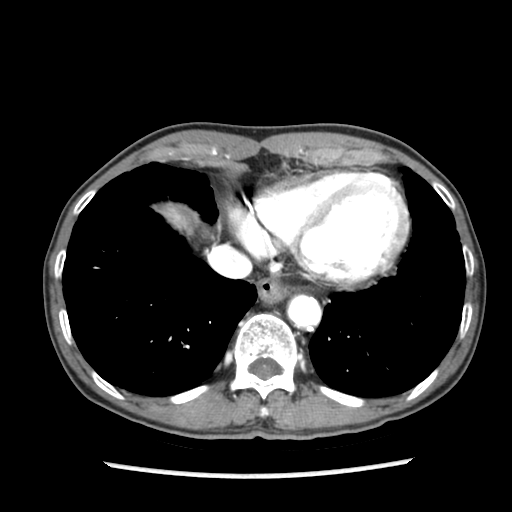
Contrast-enhanced abdominal CT (liver protocol), one axial slice; position 76 of 87 along the scan axis; reconstruction kernel STANDARD; 140 kVp; soft-tissue window (W 400 / L 40 HU); 2.5 mm slice thickness; 512 × 512 image matrix. From the clinical record (not read from this slice): diagnosis: hepatocellular carcinoma (patient treated with transarterial chemoembolisation; whether this scan precedes or follows treatment is not stated here); TNM stage (as recorded): Stage-IIIB; Child-Pugh class: A; tumour differentiation: well differentiated; tumour nodularity: uninodular.
Annotated regions visible in this slice (semi-automatically segmented with operator editing):
- abdominal aorta: box from (x=289, y=297) to (x=320, y=327) px
- liver parenchyma outside the tumour (the mass and vessels are separate outlines, so this box may not span the whole liver): (x=166, y=208)–(x=186, y=226)